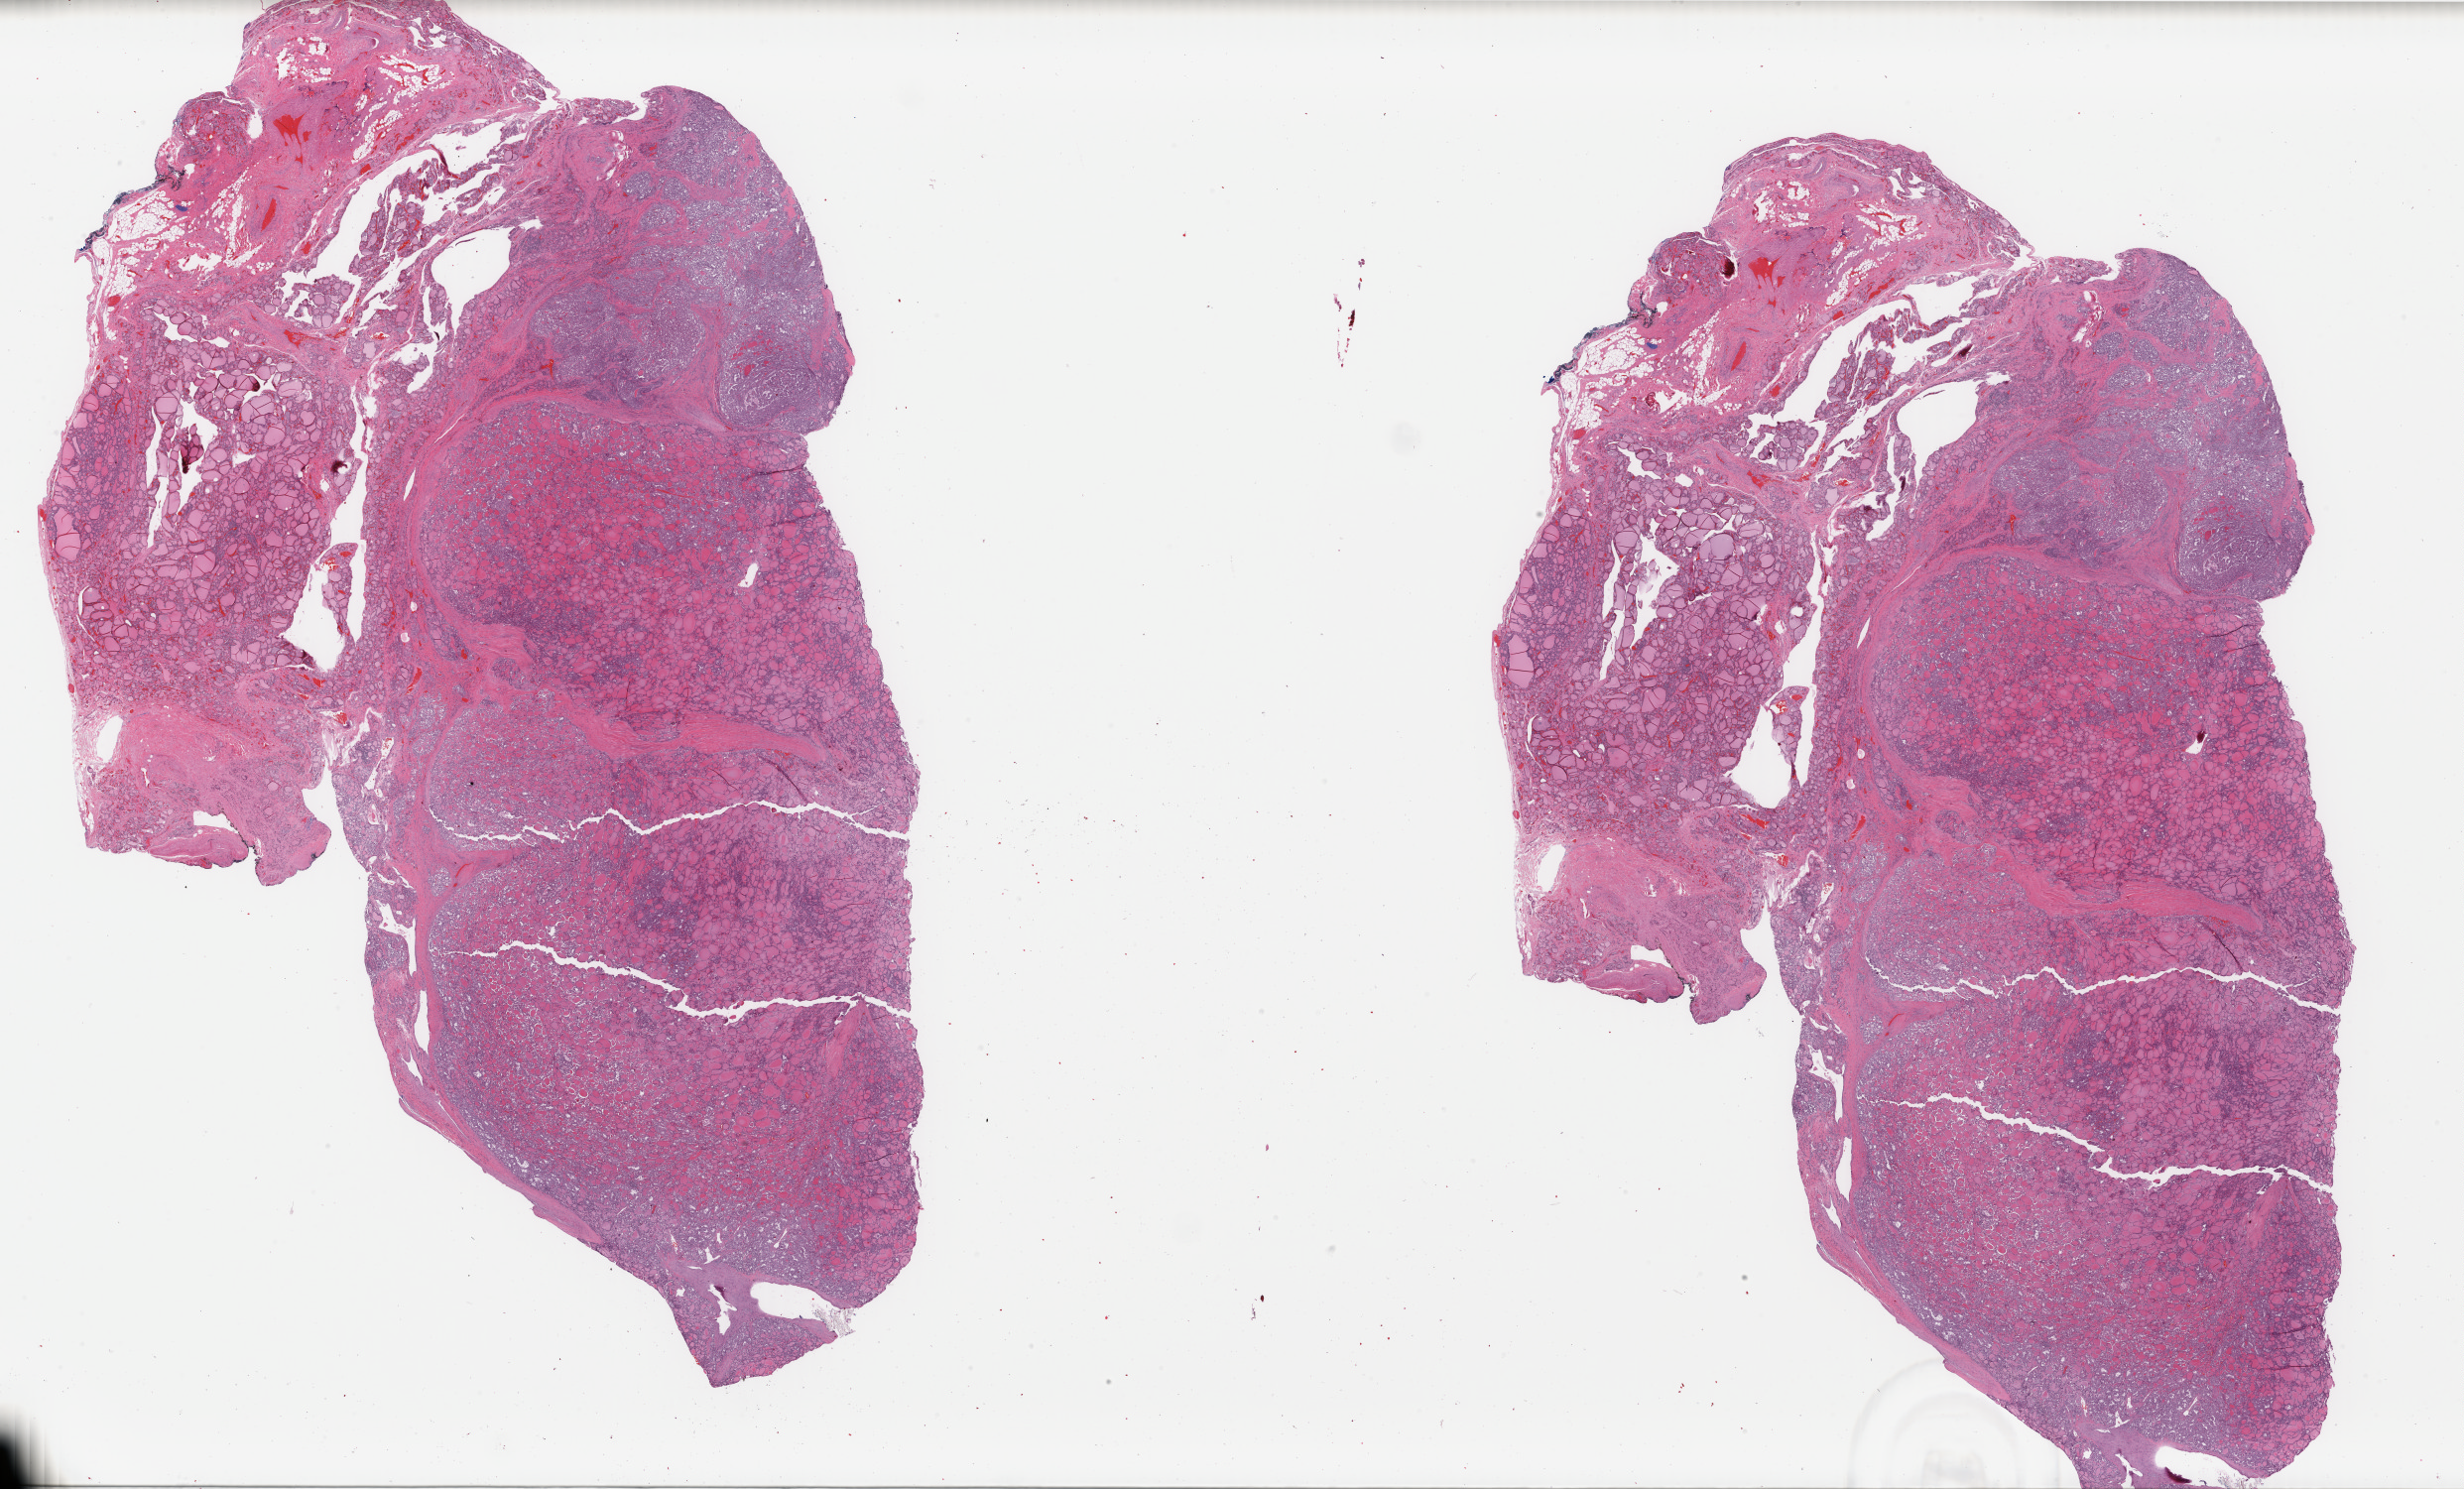
H&E whole-slide image — whole scanned area (about 39.4 x 23.8 mm, acquisition: 40x scan) shown as a low-resolution overview, FFPE section, primary tumour sample from the thyroid. Female patient; age at initial diagnosis 70 years.
AJCC pathologic stage: II (7th edition). Diagnosis: Papillary adenocarcinoma, NOS (thyroid gland).